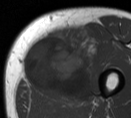
MRI of an extremity soft-tissue mass, one axial slice. Slice 23 of 55 in the series (ordered by position). MR volume resampled by the dataset authors to the PET/CT grid (not the native acquisition matrix). 3.27 mm slice thickness. 131 × 118 image matrix. Male patient. Case-level facts recorded for this patient, not image findings: histological type: pleiomorphic liposarcoma; grade: high; site of the primary tumour: left thigh.
Annotated regions visible in this slice (expert contour drawn on MRI and transferred to this co-registered scan by the dataset authors):
- gross tumour volume including surrounding oedema: bounding box <21,23,101,104> (left, top, right, bottom; pixels)
- gross tumour volume (mass): <21,34,92,99>